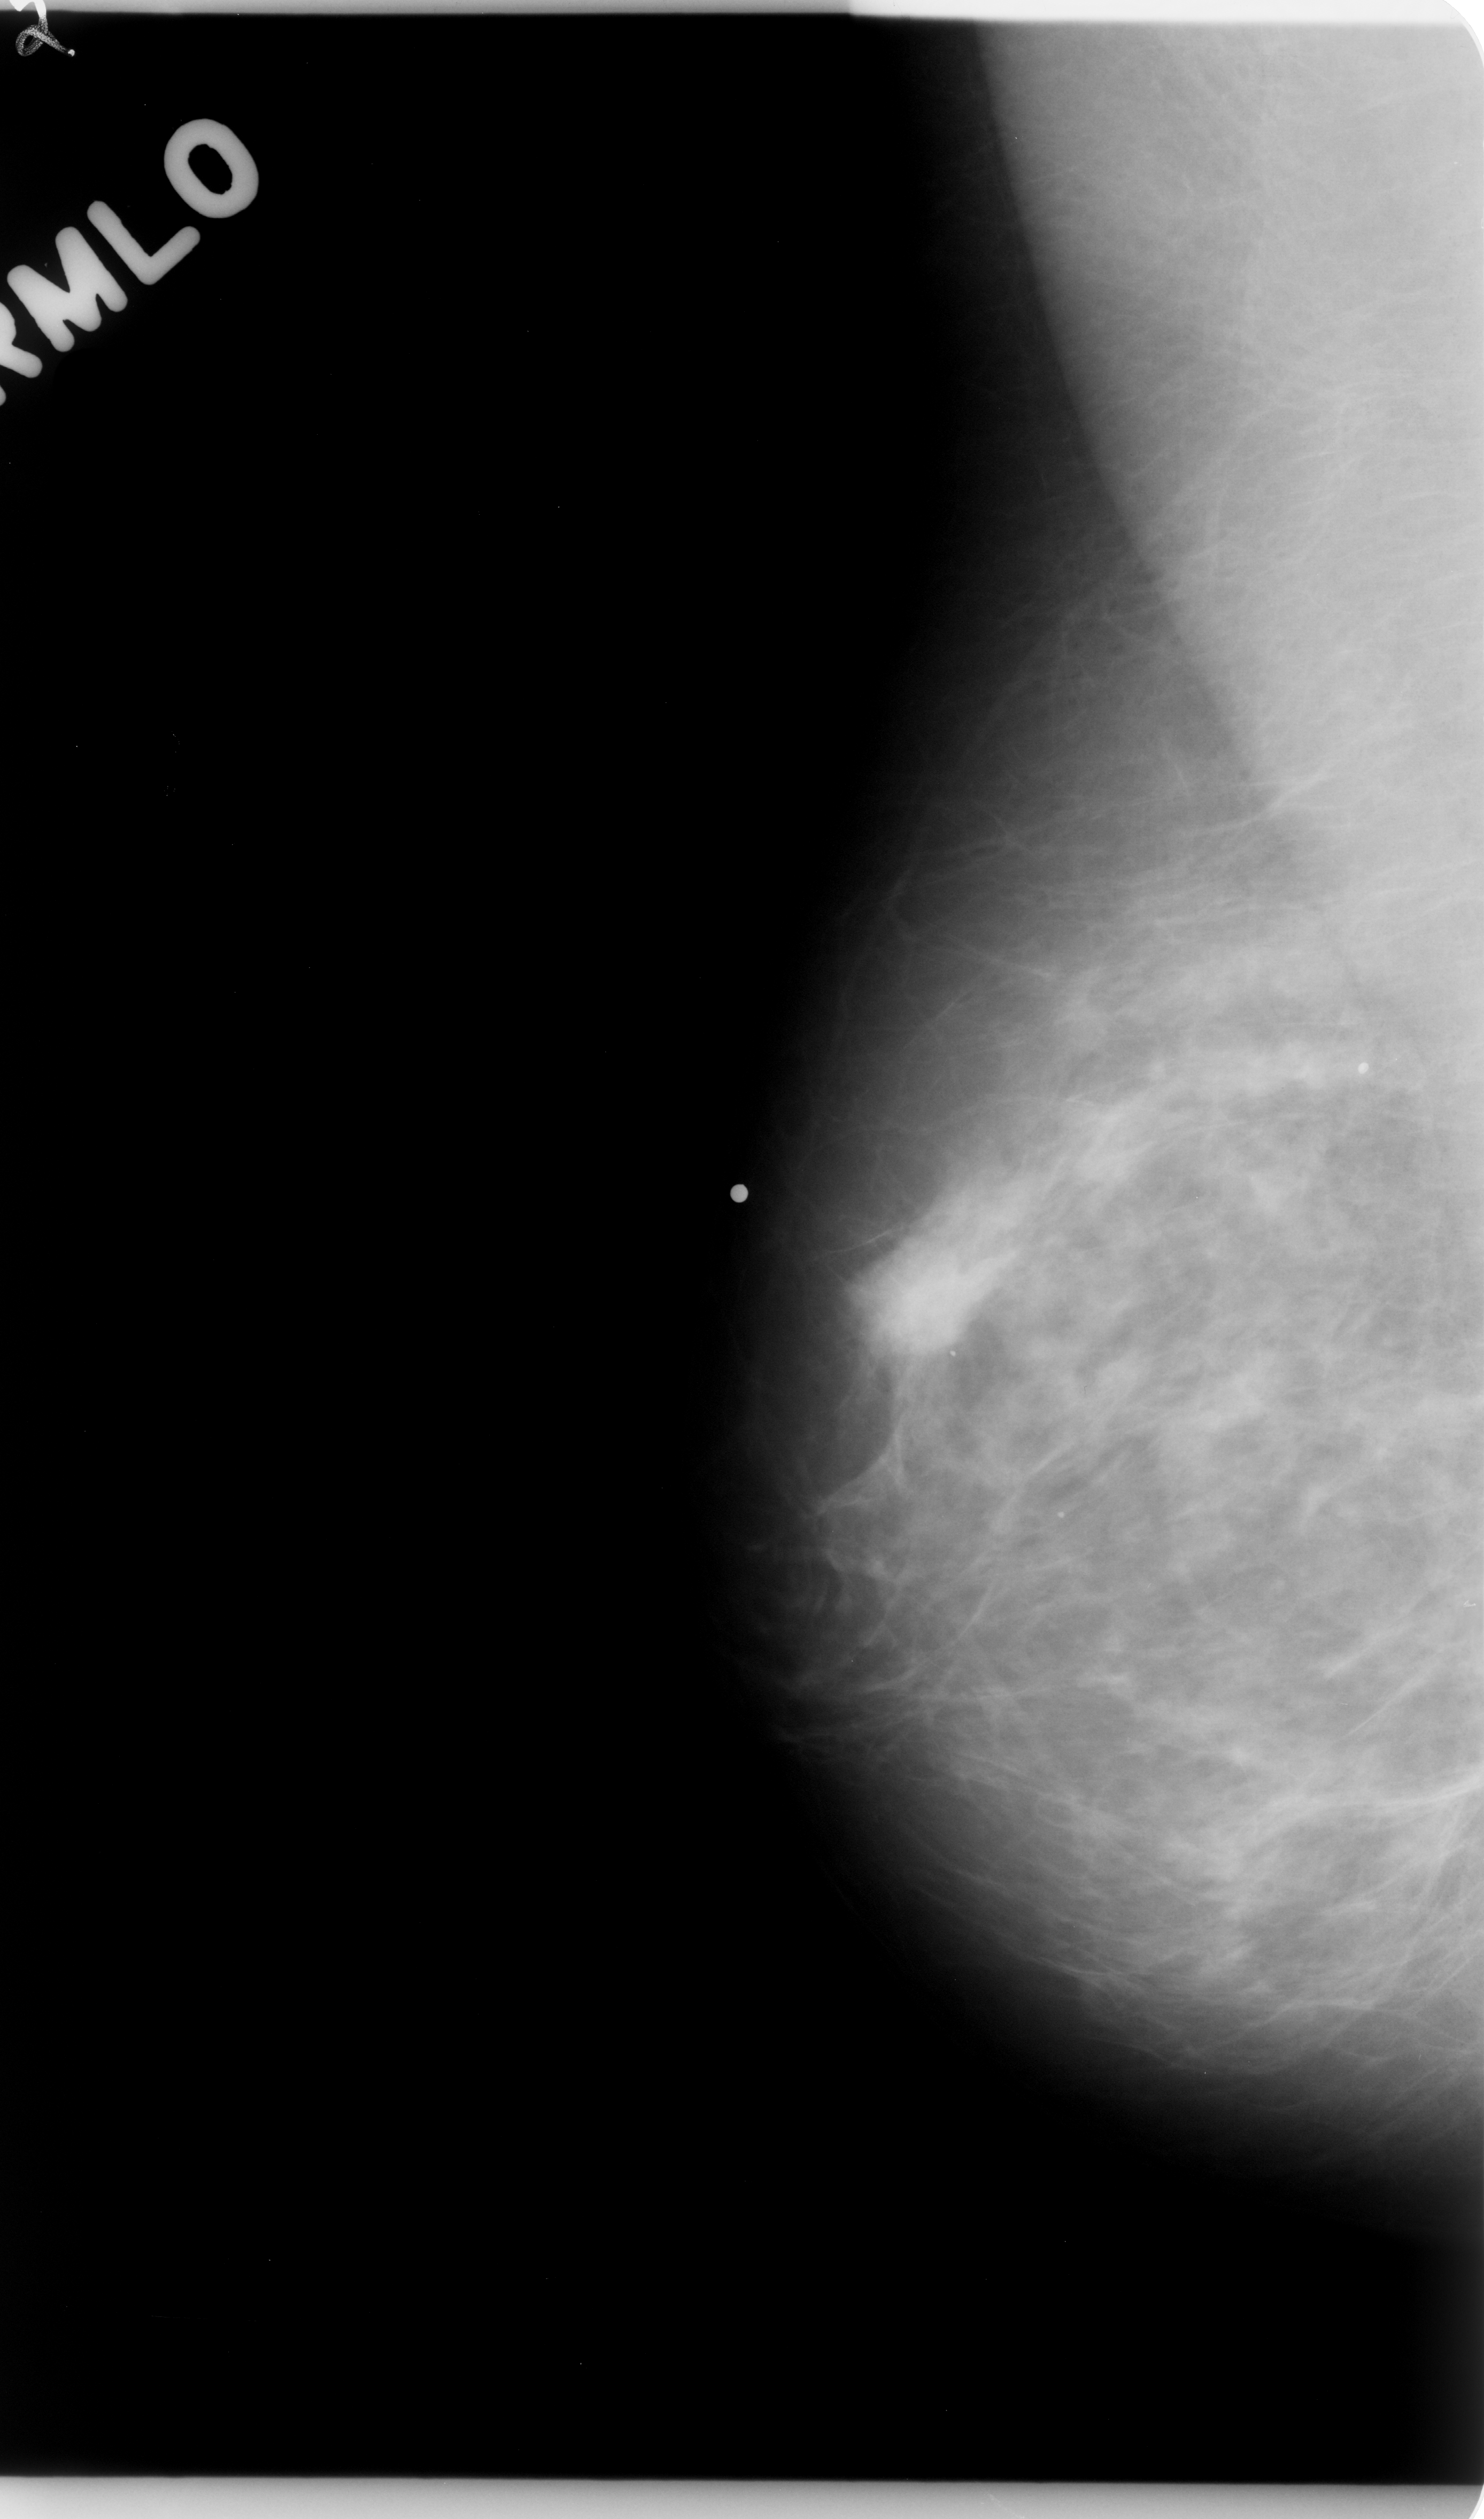
Scanned film-screen mammogram; right breast; mediolateral oblique (MLO) view; BI-RADS breast density category 2 (scale 1–4); 1484 × 2519 image matrix.
Expert-marked regions of interest on this film, with their recorded descriptors:
- mass, shape irregular, margins microlobulated; BI-RADS assessment category 5; subtlety rating 5 on a 1 (subtle) to 5 (obvious) scale; pathology result (as recorded, not read from the image): malignant: bounding box [x1, y1, x2, y2] px = [837, 1214, 1003, 1386]